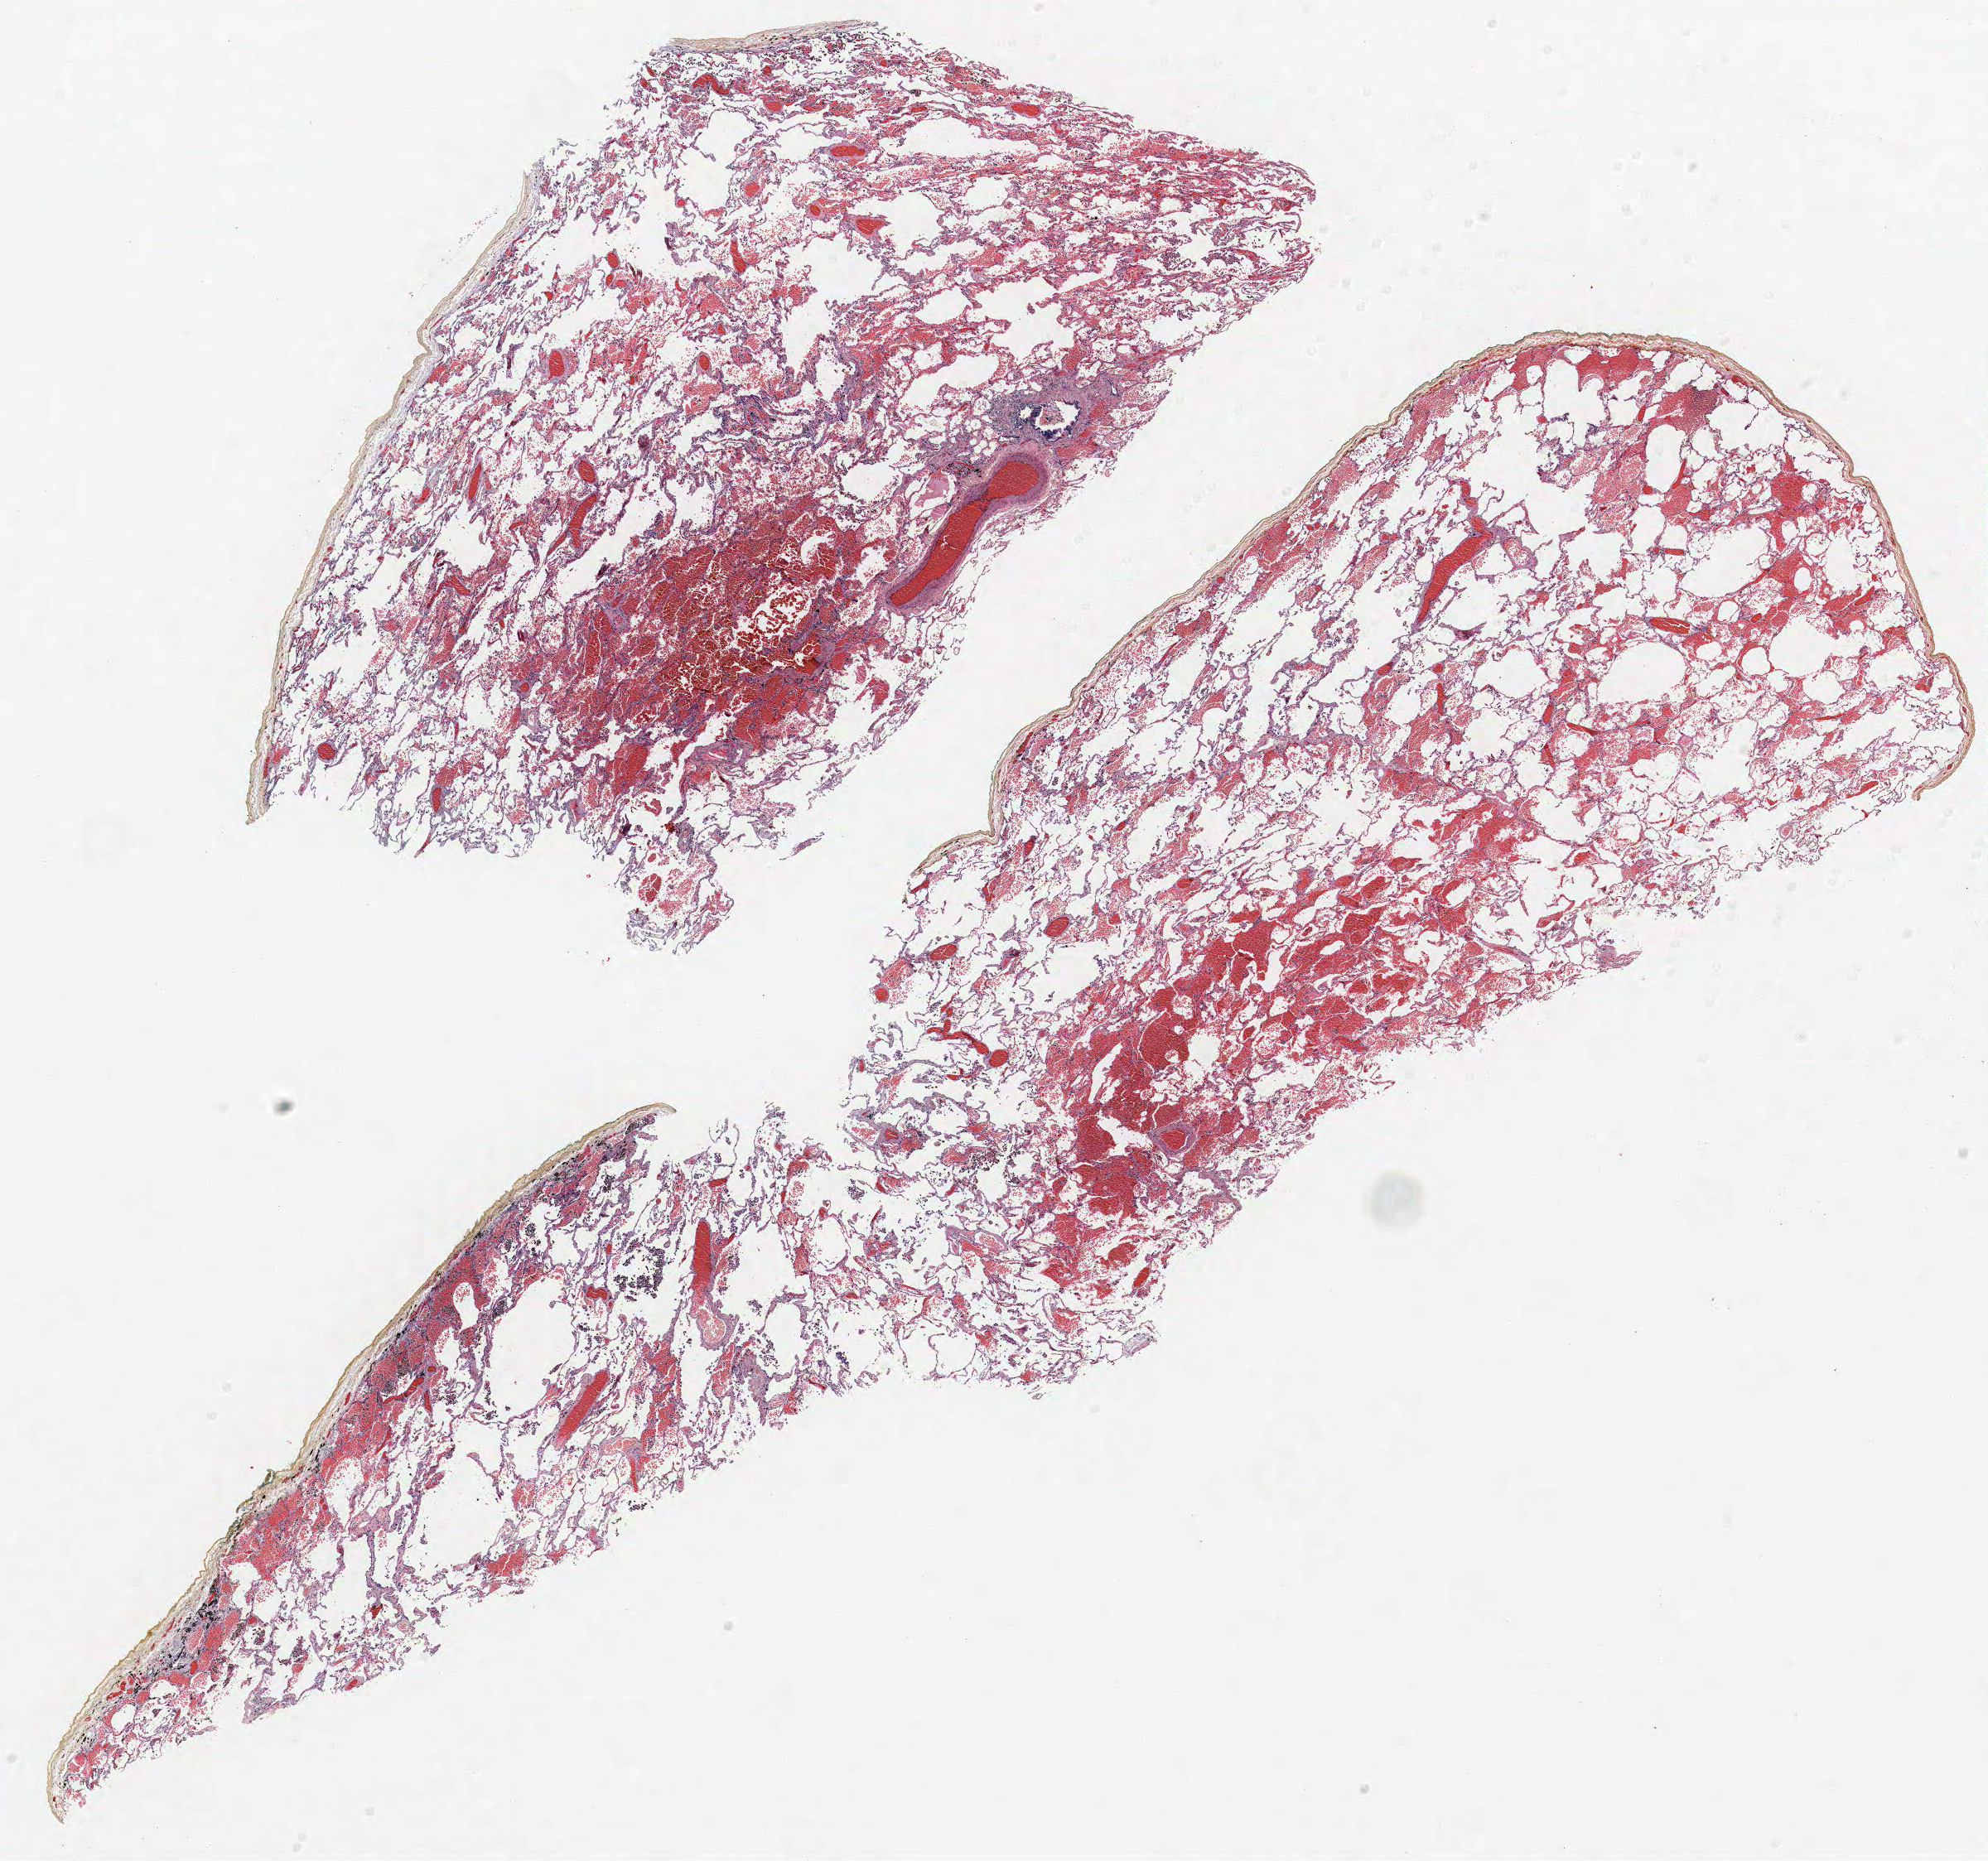
Whole-slide histology image, H&E, a low-resolution overview of the entire scanned area, about 19.2 x 18.0 mm (from a 40x scan), FFPE section, lung tissue. Male, age 63 at enrolment. Current smoker at enrolment. Grade: moderately differentiated (G2).
* stage (AJCC 6th edition): IA
* participant's lung-cancer diagnosis: Adenocarcinoma, NOS
* primary tumour location (clinical record): right lower lobe
* tumour size (pathology): 12 mm
* note: participant had 3 primary lung cancers recorded; fields above describe the first